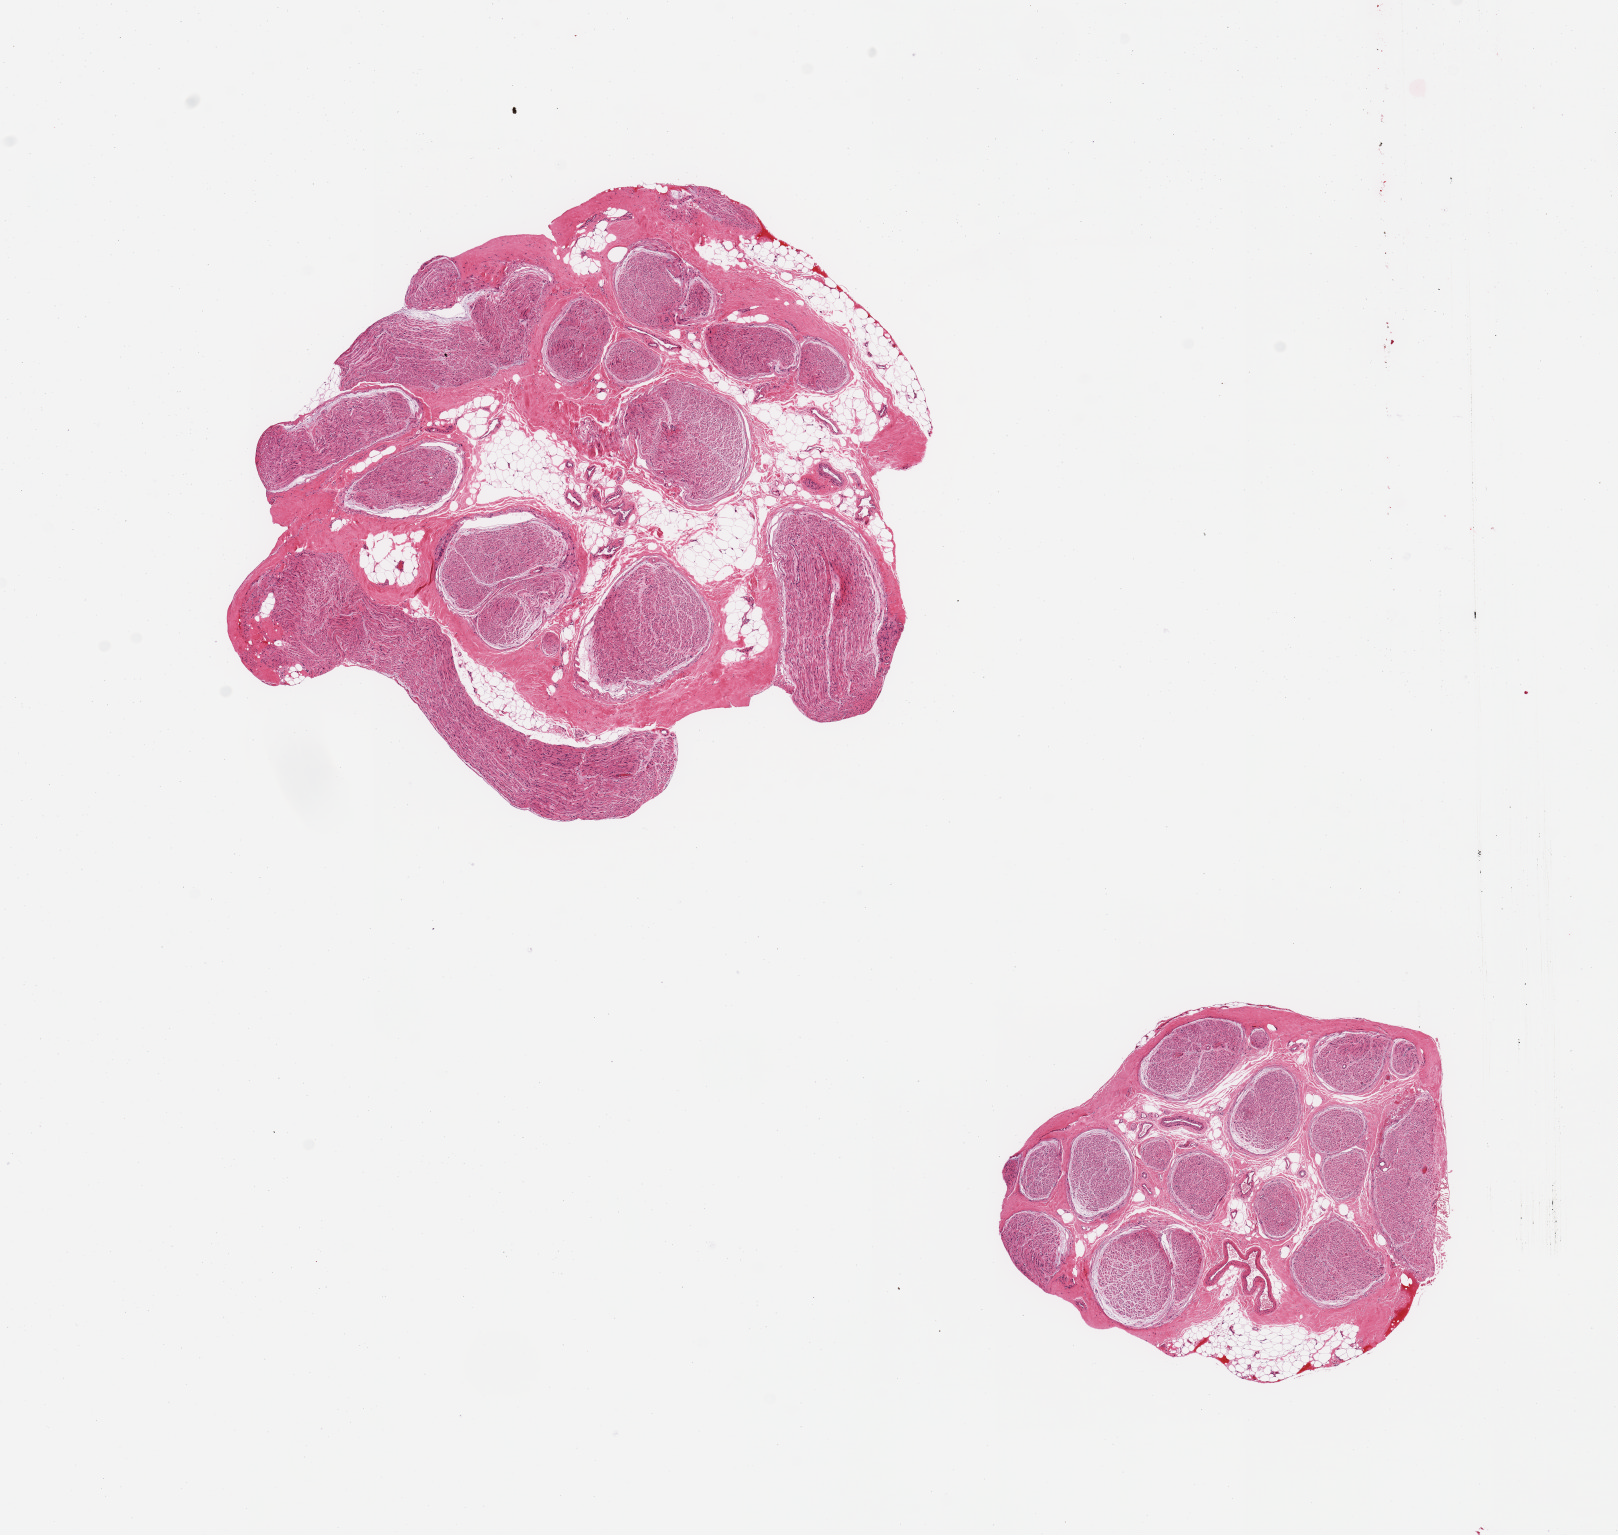
Hematoxylin and eosin (H&E) whole-slide image, a low-resolution overview of the entire scanned area, about 12.8 x 12.1 mm, PAXgene-fixed, paraffin-embedded tissue, target tissue: tibial nerve, donor tissue sample.
Reviewer comment on this tissue sample: 2 pieces, no significant adherent fat.